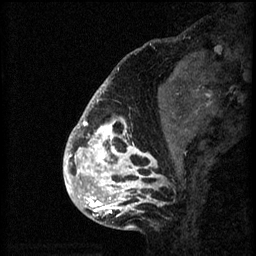
Breast MRI (dynamic contrast-enhanced), one sagittal slice; slice 19 of 60 in the series (ordered by position); 3 images stored at this slice position (order not interpretable as contrast timing); 1.5 T; TE 4.2 ms, TR 8.2 ms; 2 mm slice thickness; 256 × 256 image matrix, field of view 180 × 180 mm. Patient: female, 41 years.
Structures marked on this image (semi-automatic segmentation, software-assisted and operator-edited):
- analysis volume of interest (the breast-tissue region the enhancement analysis was run in; not a lesion): bounding box [x1, y1, x2, y2] px = [72, 108, 176, 205]
- tumour enhancement mask (voxels above the 70 % enhancement threshold inside the analysis volume of interest): [72, 108, 164, 205]